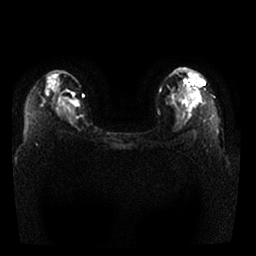
Breast MRI, one axial slice; slice 23 of 29 in the series (ordered by position); diffusion-weighted series; image 2 of 4 stored at this slice position (different b-values; order by instance number); 1.5 T; 4 mm slice thickness; 256 × 256 image matrix, field of view 340 × 340 mm. Female patient.
Annotated regions visible in this slice (expert manual segmentation):
- tumour on diffusion-weighted imaging: bounding box [x1, y1, x2, y2] px = [72, 100, 79, 105]